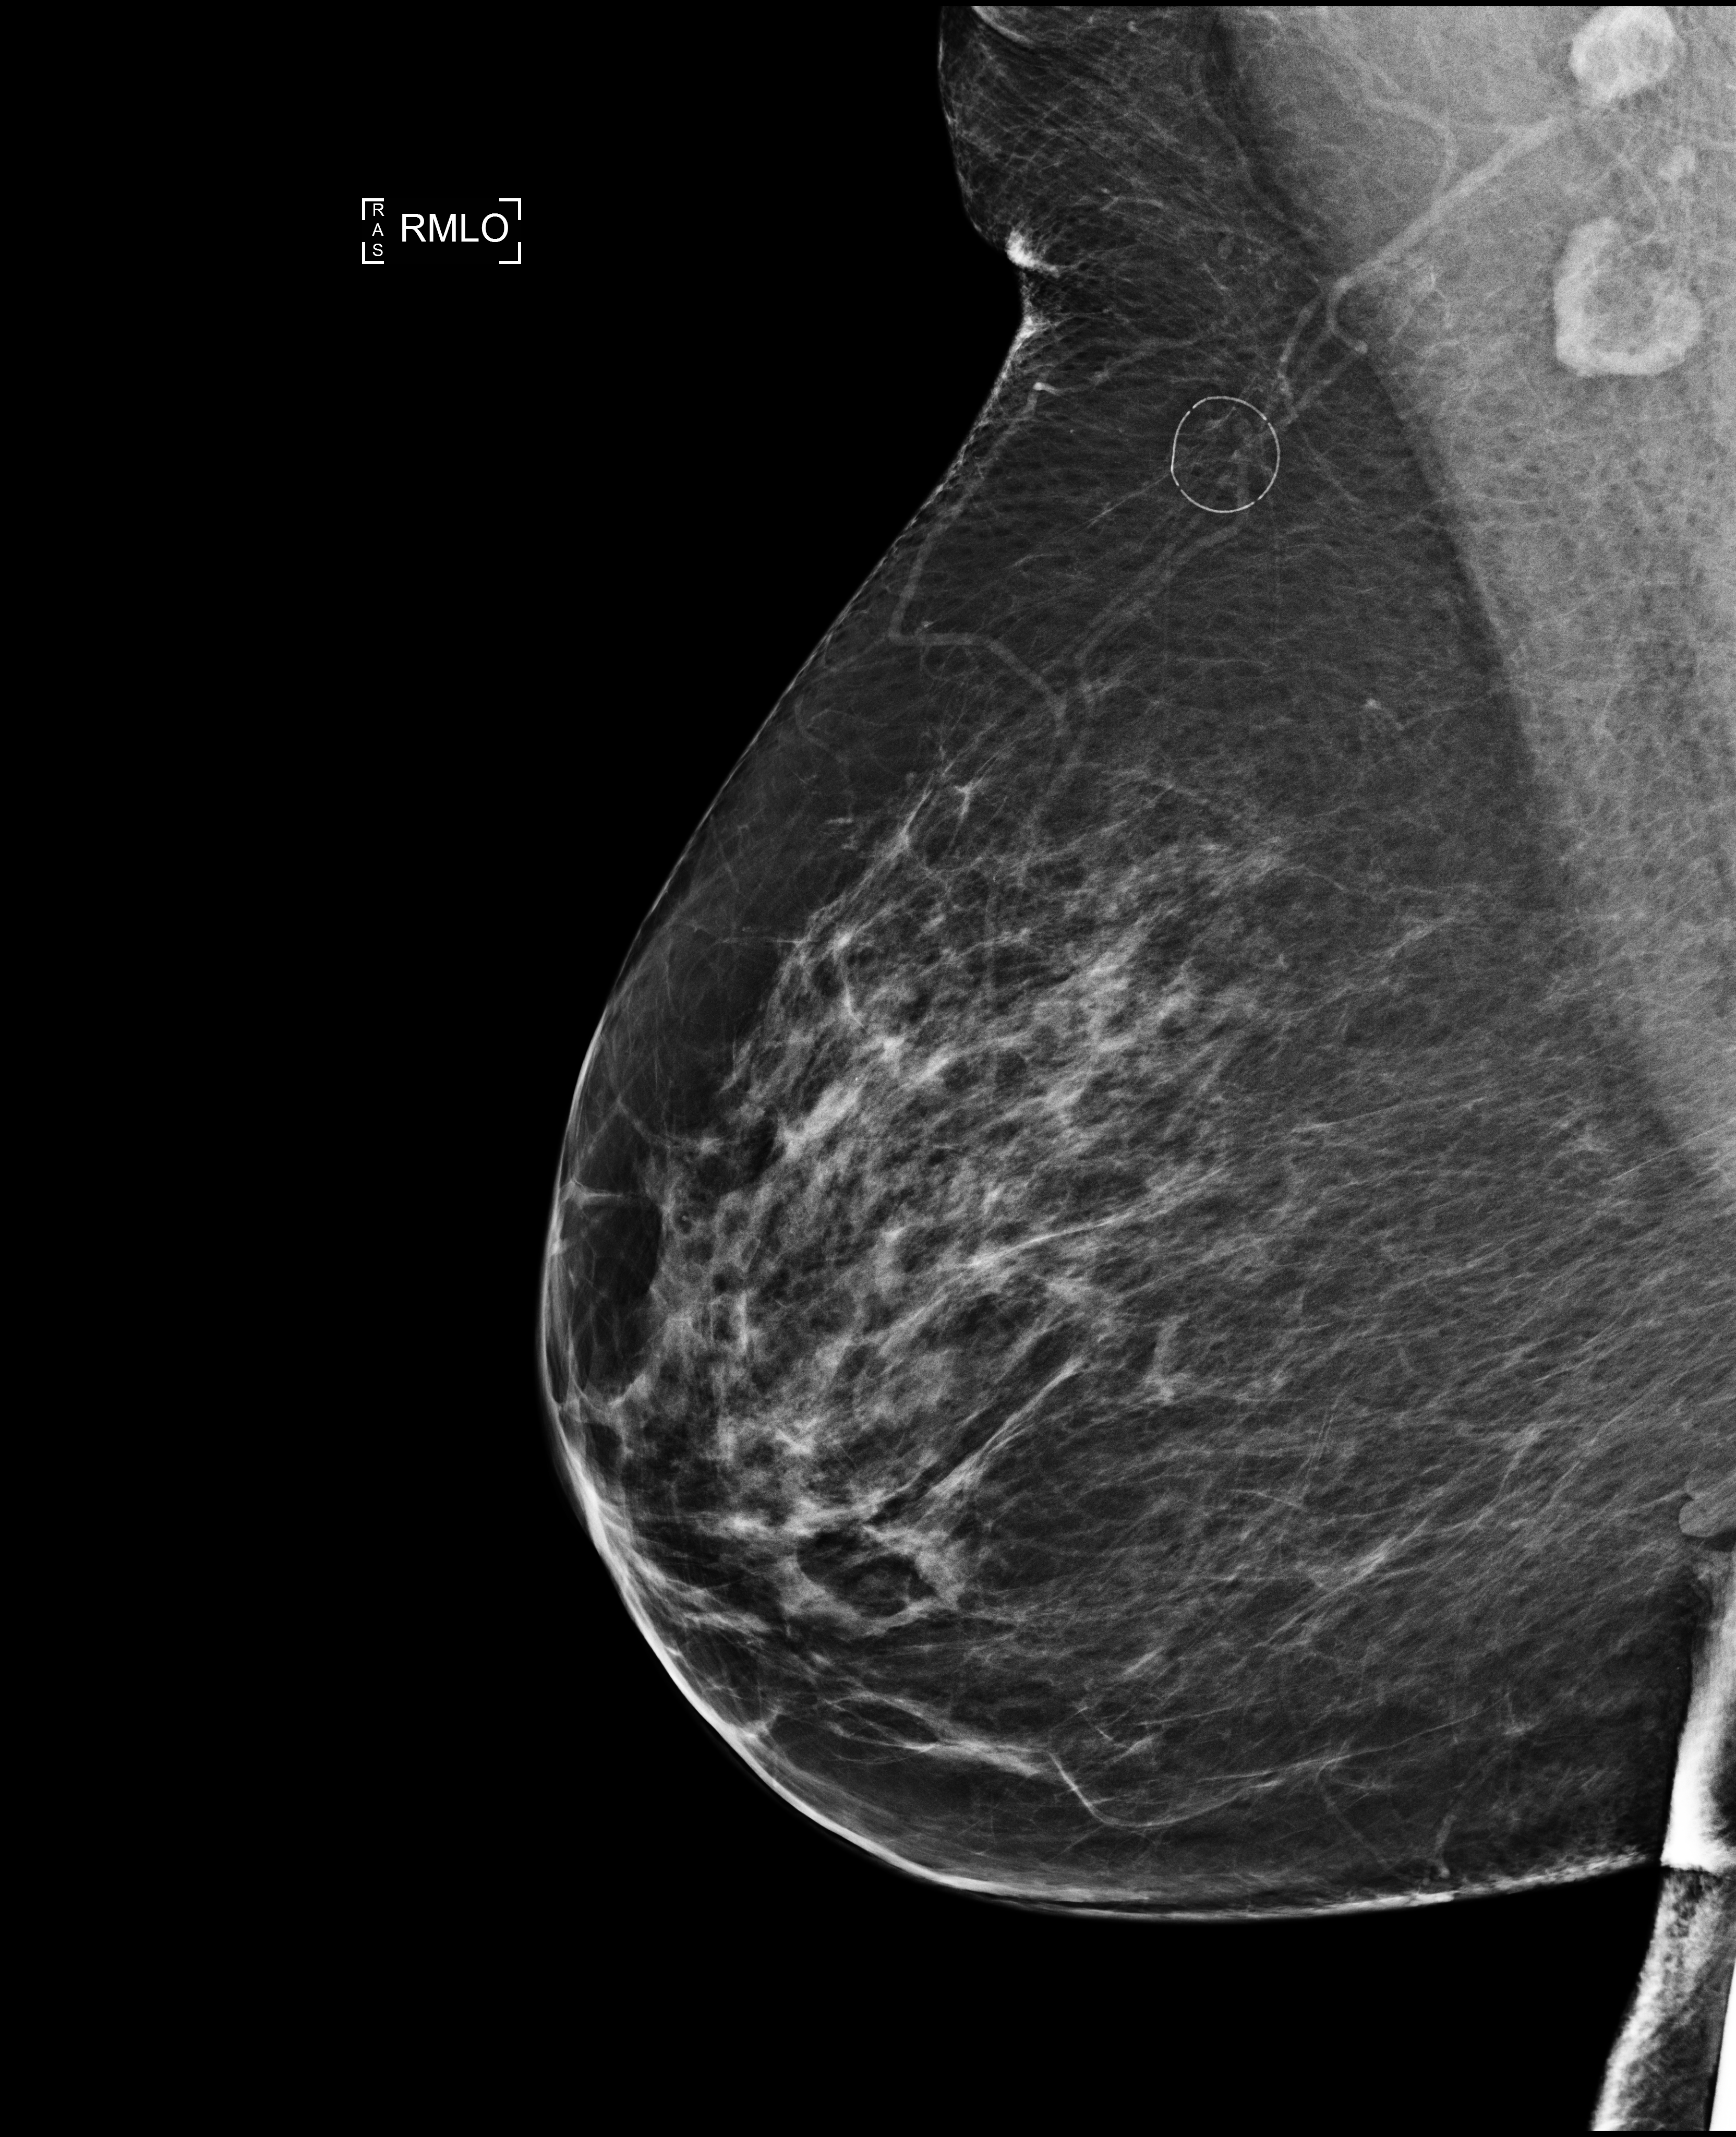
Full-field digital mammogram (FFDM), right breast, mediolateral oblique (MLO) view, annual screening mammography examination, compressed breast thickness 76 mm, system: Selenia Dimensions. Female patient, age 66 years.
Breast density at the screening exam (both breasts): scattered fibroglandular densities (BI-RADS density category b).